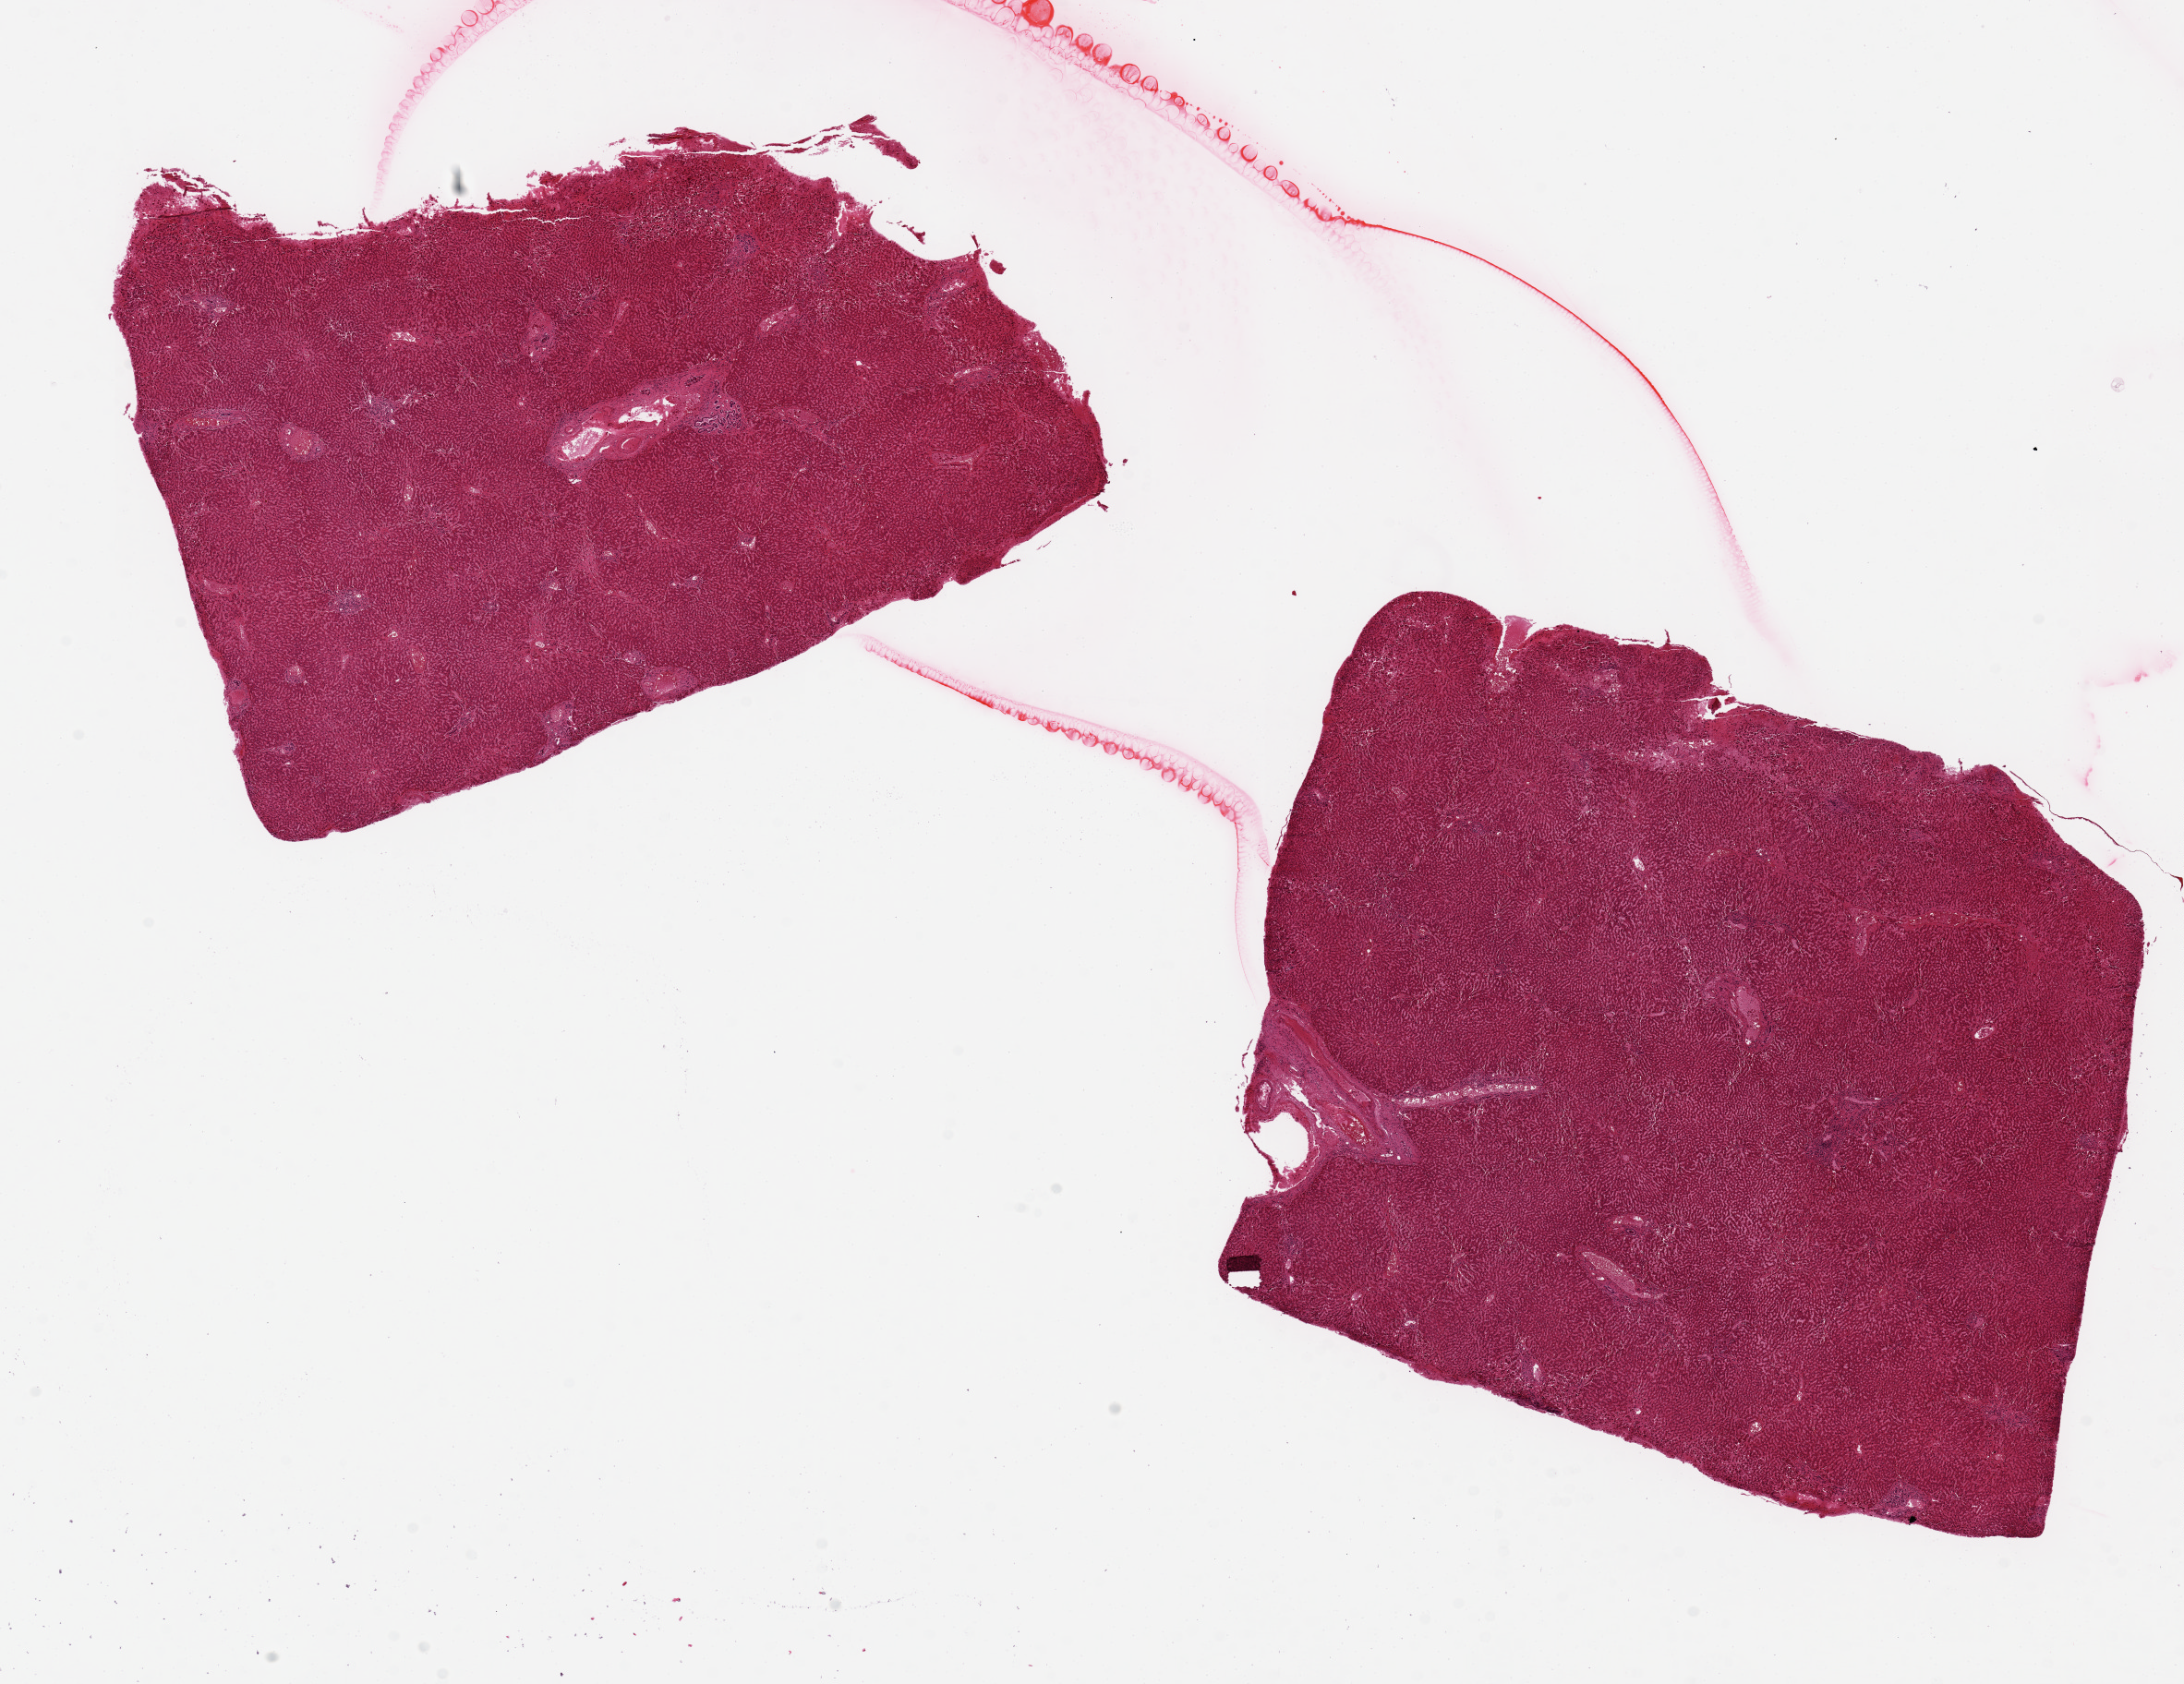
Digitized haematoxylin and eosin-stained section, brightfield, a low-resolution overview of the entire scanned area, about 18.7 x 14.4 mm (from a 20x scan), PAXgene-fixed, paraffin-embedded tissue, target tissue: liver, donor tissue sample. Male donor.
Reviewer comment on this tissue sample: 2 pieces, ~8x6mm.